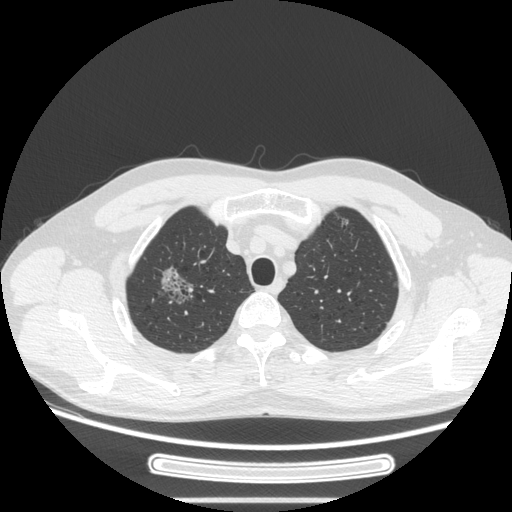
Chest CT, one axial slice; position 221 of 269 along the scan axis; 120 kVp; lung window (W 1500 / L -600 HU); 1.25 mm slice thickness; 512 × 512 image matrix, field of view 382 × 382 mm. Patient: male, 53 years. Case-level facts recorded for this patient, not image findings: clinical TNM (as recorded): T1c N0 M0; histopathological grade: G2.
Outlined on this slice (bounding box drawn by a radiologist):
- lung tumour (recorded histology: adenocarcinoma): bounding box (x1, y1, x2, y2) in pixels: (150, 260, 207, 317)